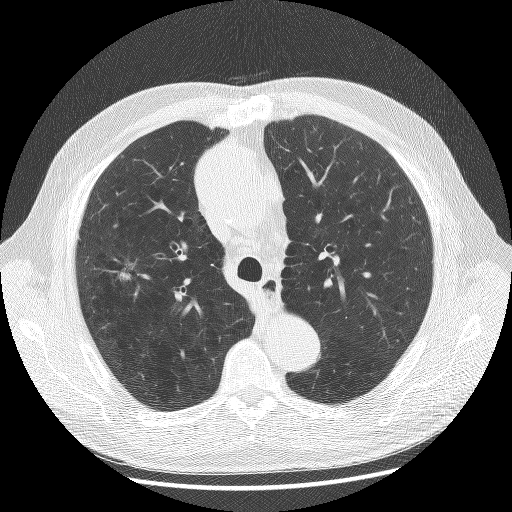
Low-dose screening chest CT, axial slice; baseline screening round; lung window (W 1500 / L -600 HU); 2.5 mm slice thickness; 120 kVp; slice 48 of 175 in the series; 512 × 512 image matrix. Male participant, aged 70 years at enrolment. Current smoker at enrolment.
Expert reader's lesion annotation, bounding box (x1, y1, x2, y2) in pixels: (73, 240, 149, 308). The screening reader recorded 2 non-calcified nodules or masses ≥4 mm on this exam; which of them this box marks is not recorded. Official screen result: positive, change unspecified: nodule(s) >= 4 mm or enlarging nodule(s), mass(es), or other non-specific abnormalities suspicious for lung cancer. Later outcome: lung cancer diagnosed 23 days after this screen — non-small cell carcinoma, right upper lobe, poorly differentiated (G3), stage IA (AJCC 6th edition), 20 mm at pathology.